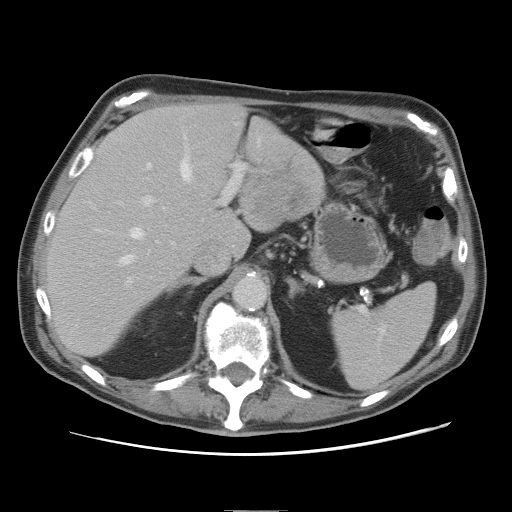
Contrast-enhanced abdominal CT, one axial slice; soft-tissue window (W 400 / L 40 HU); 5 mm slice thickness; 512 × 512 image matrix, field of view 375 × 375 mm. Male patient, age 69 years. From the clinical record (not read from this slice): diagnosis: colorectal cancer liver metastases, imaged before liver resection; multiple liver metastases: no; largest metastasis: 8.5 cm; disease in both lobes: no.
Structures marked on this image (expert manual segmentation):
- hepatic veins: bounding box (x1, y1, x2, y2) in pixels: (121, 157, 193, 265)
- liver: (48, 104, 326, 356)
- planned liver remnant (the part of the liver to remain after resection): (48, 104, 246, 356)
- portal vein (with intrahepatic branches): (126, 140, 261, 284)
- liver metastasis: (280, 186, 306, 209)